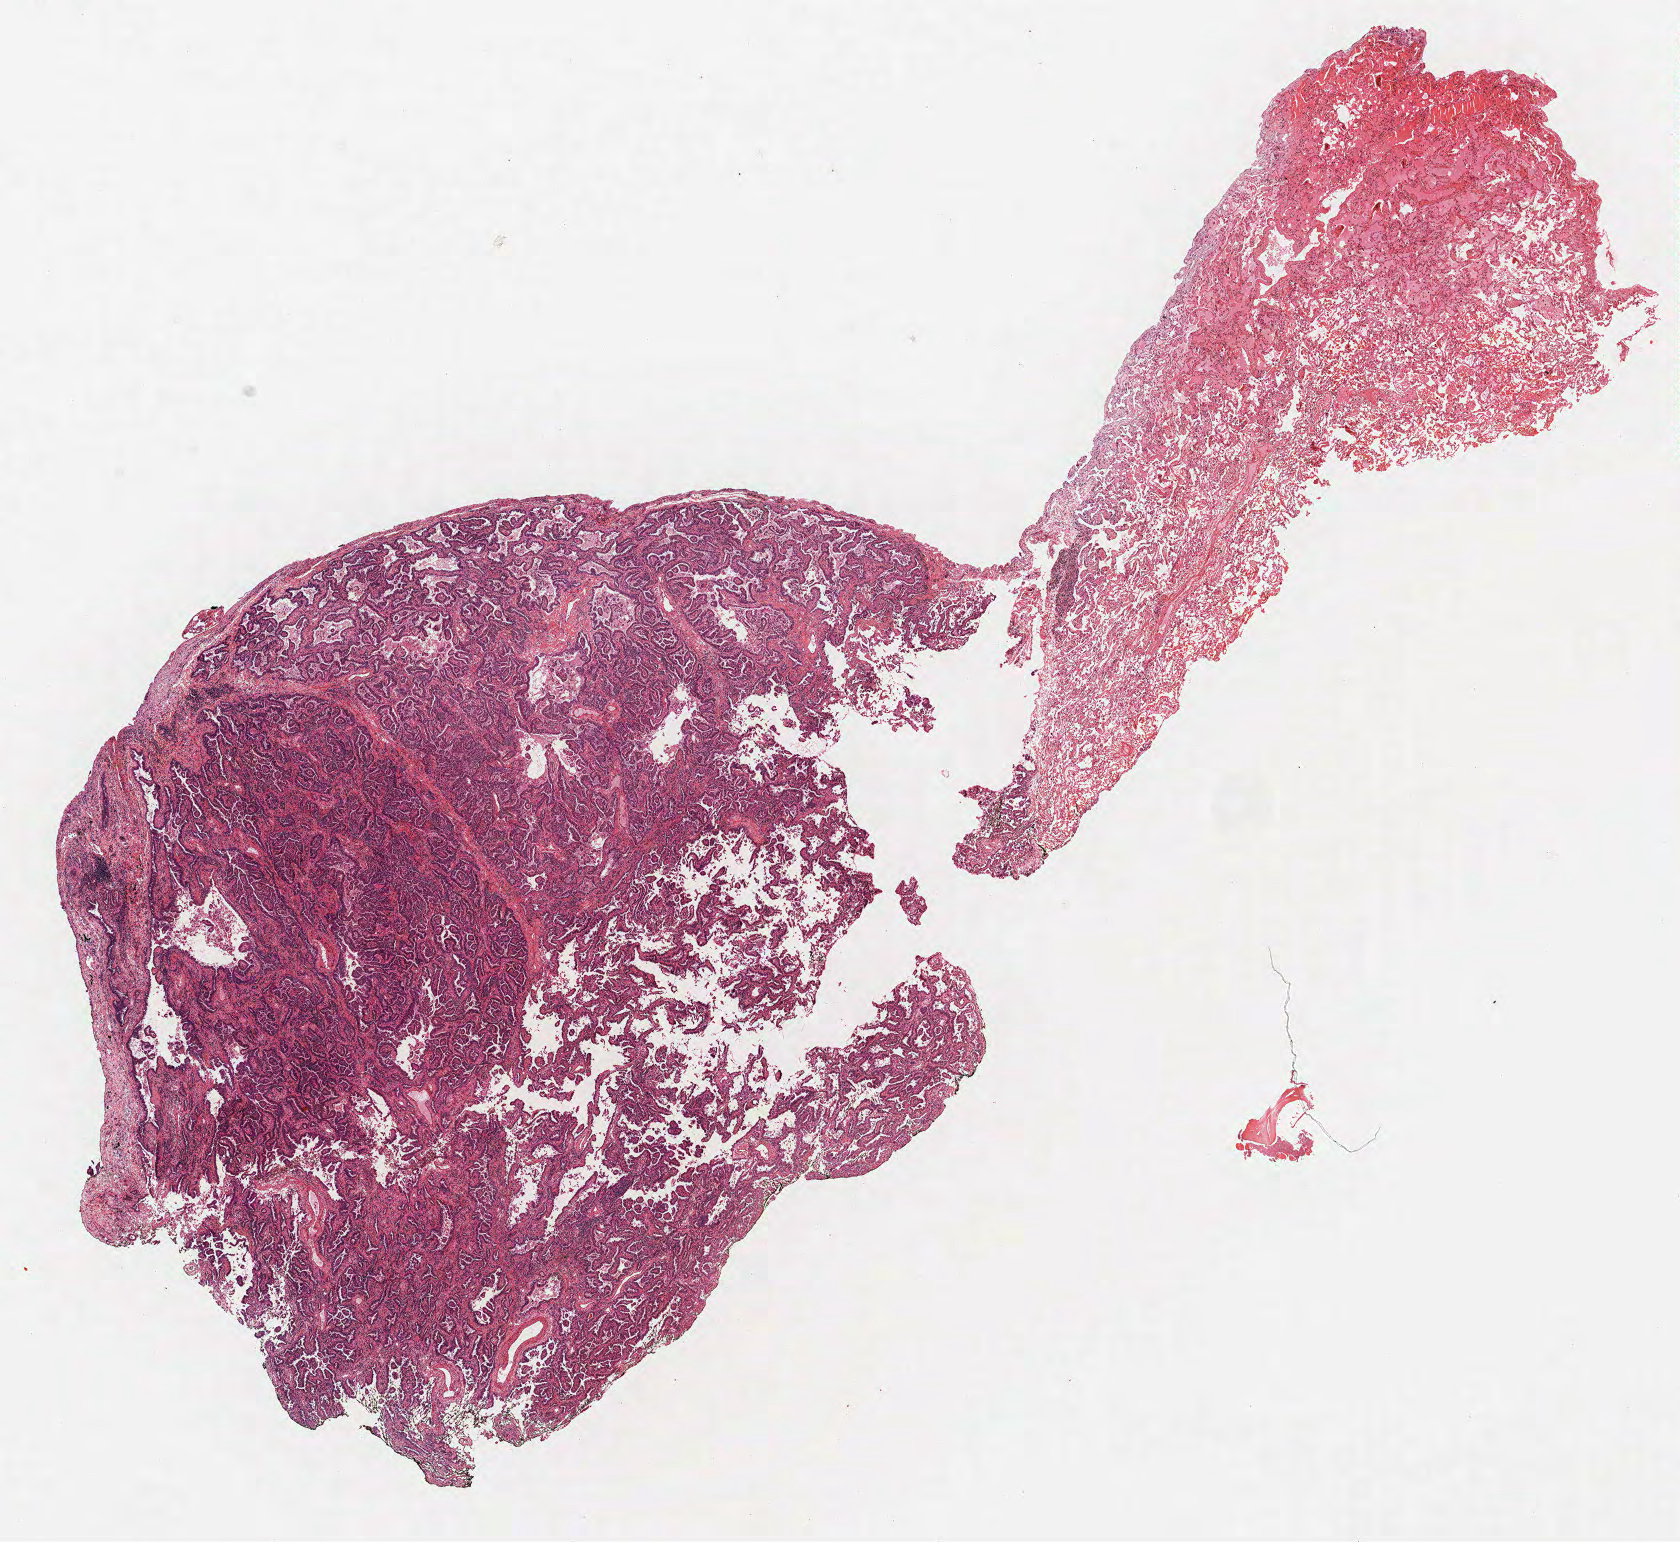
Whole-slide histology image, H&E, shown as a low-resolution overview of the whole scanned area (about 13.4 x 12.3 mm, from a 40x scan). Formalin-fixed paraffin-embedded (FFPE) section. Lung. Male patient, aged 60 at enrolment. Current smoker at enrolment. Grade: moderately differentiated (G2).
Participant's lung-cancer diagnosis: Papillary adenocarcinoma, NOS. Primary tumour location (clinical record): left lower lobe. Tumour size (pathology): 35 mm. Stage (AJCC 6th edition): IB.